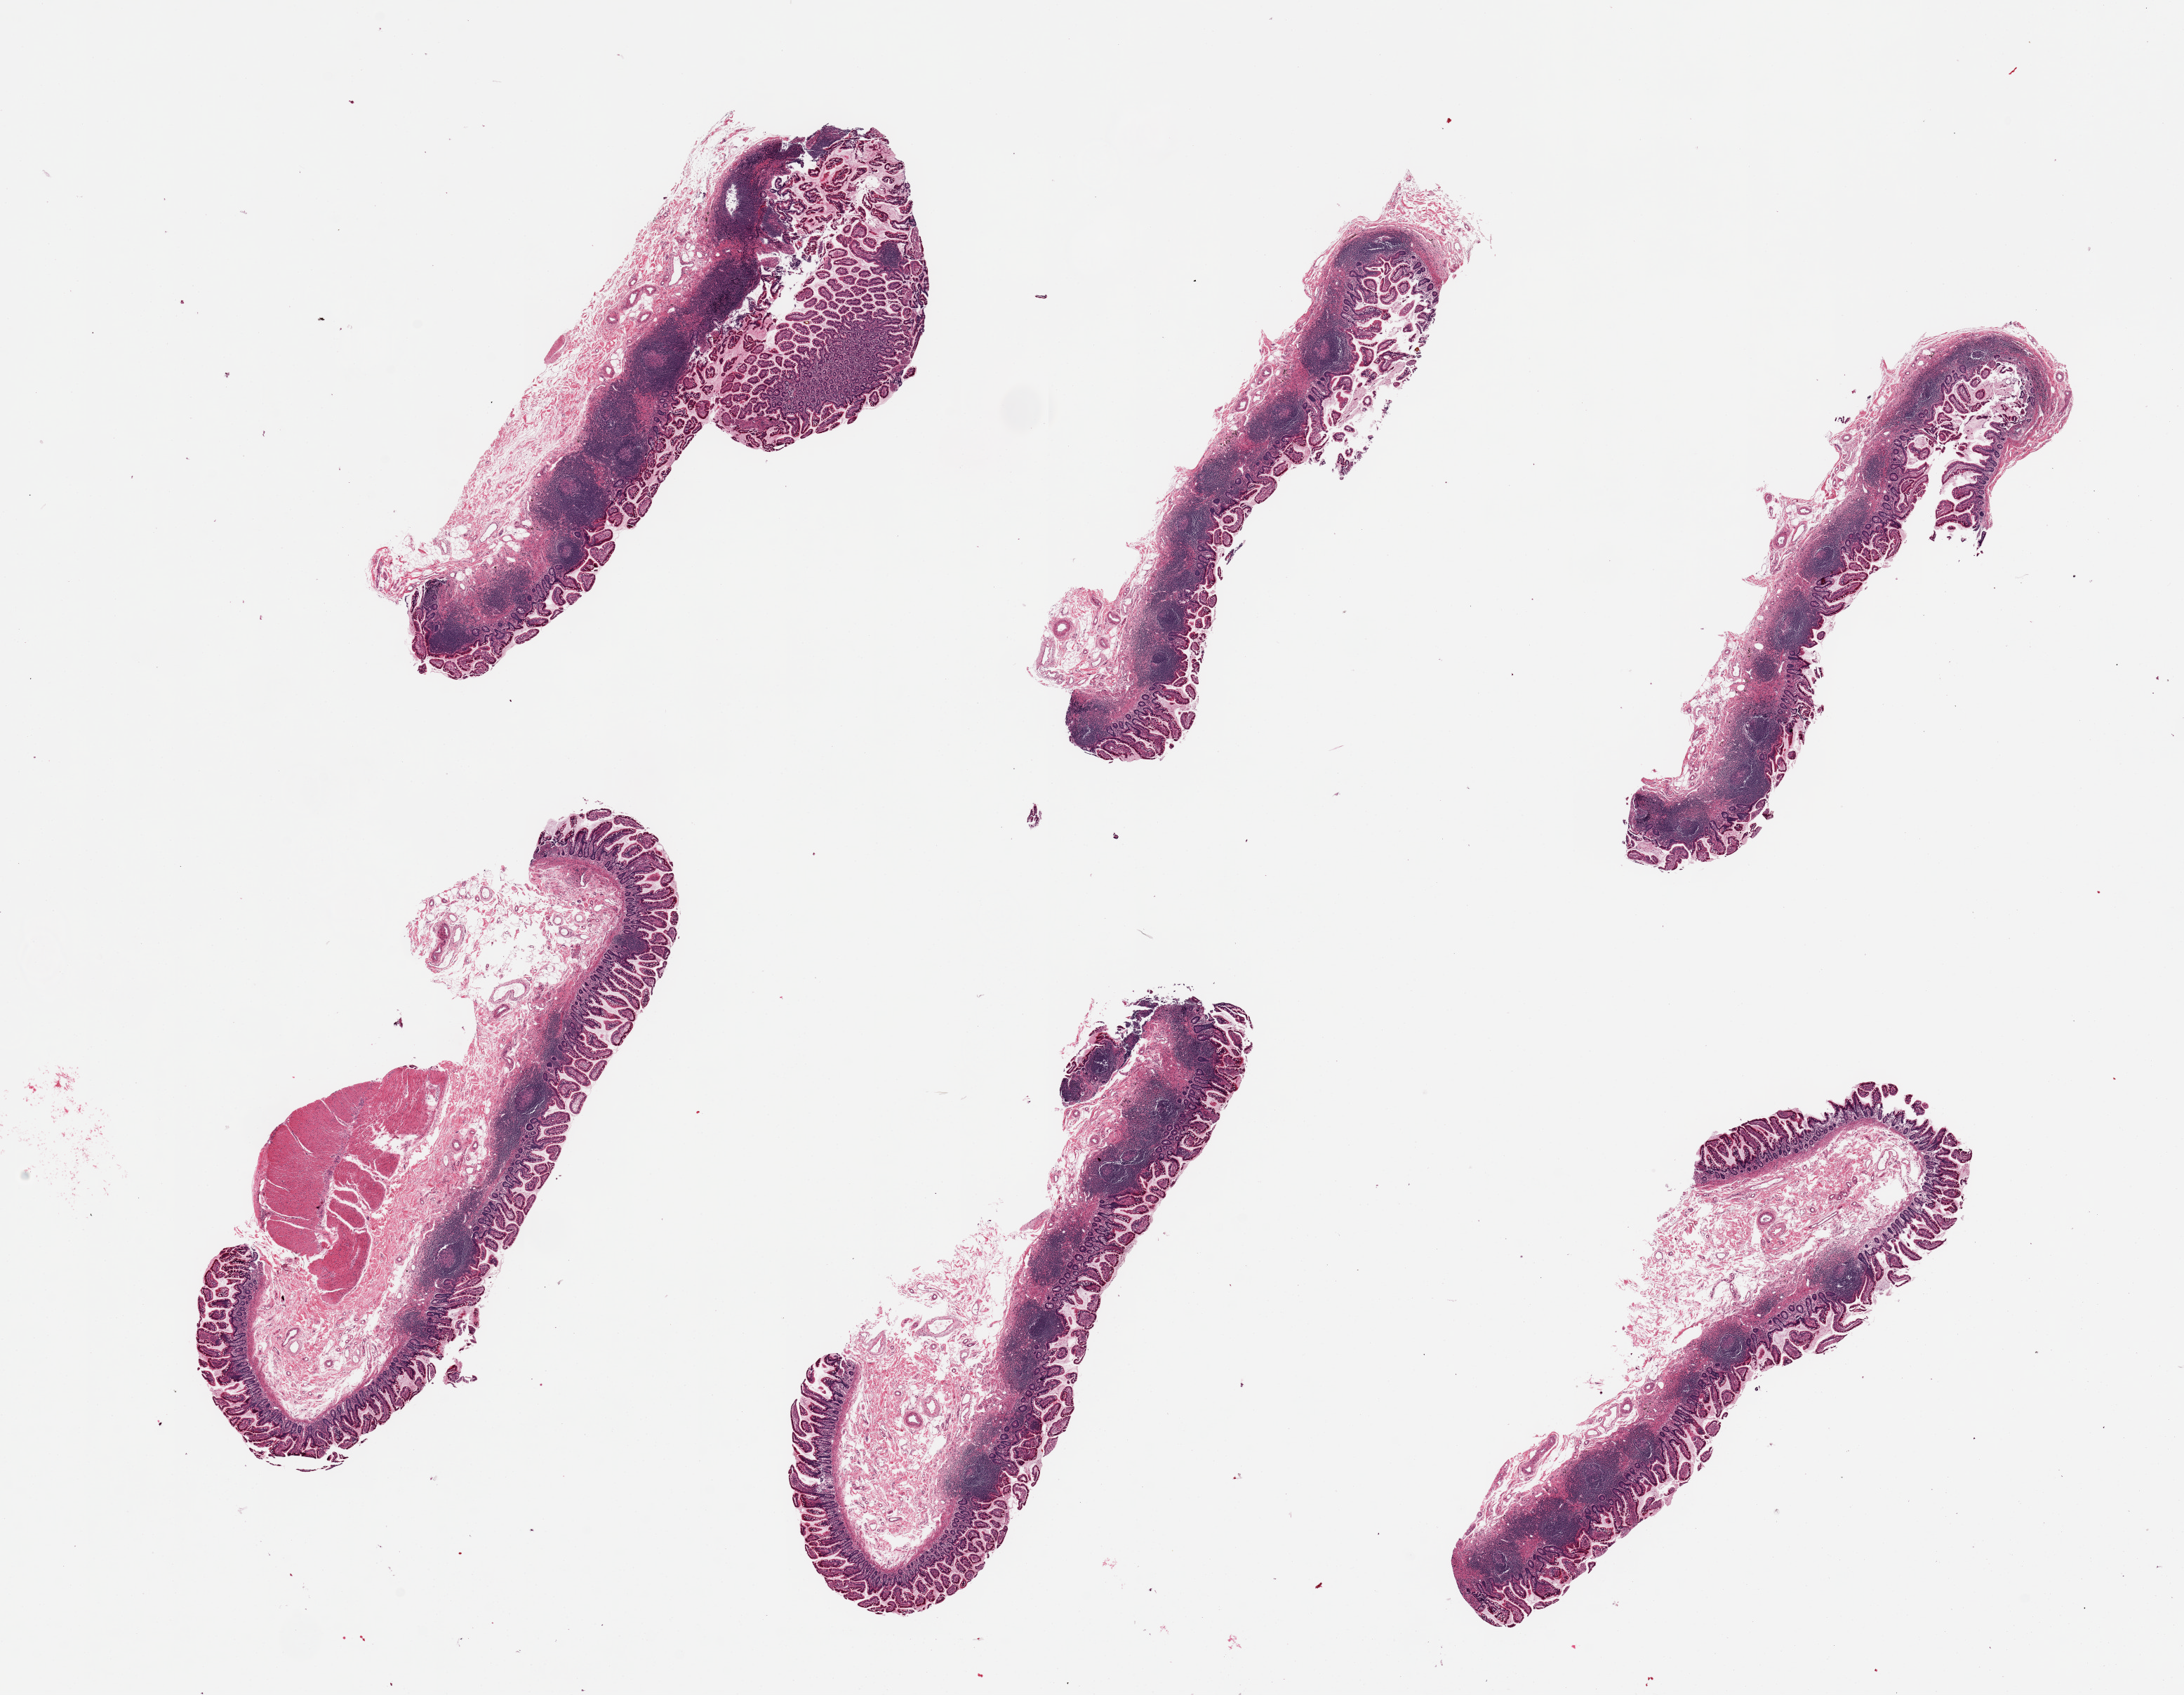
H&E whole-slide image, brightfield, shown as a low-resolution overview of the whole scanned area (about 24.6 x 19.1 mm). PAXgene-fixed, paraffin-embedded tissue. Section of ileum (target tissue). Tissue donor sample.
Review note (as recorded): 6 pieces, lymphoid tissue well represented. One piece has portion of muscularis (not target).